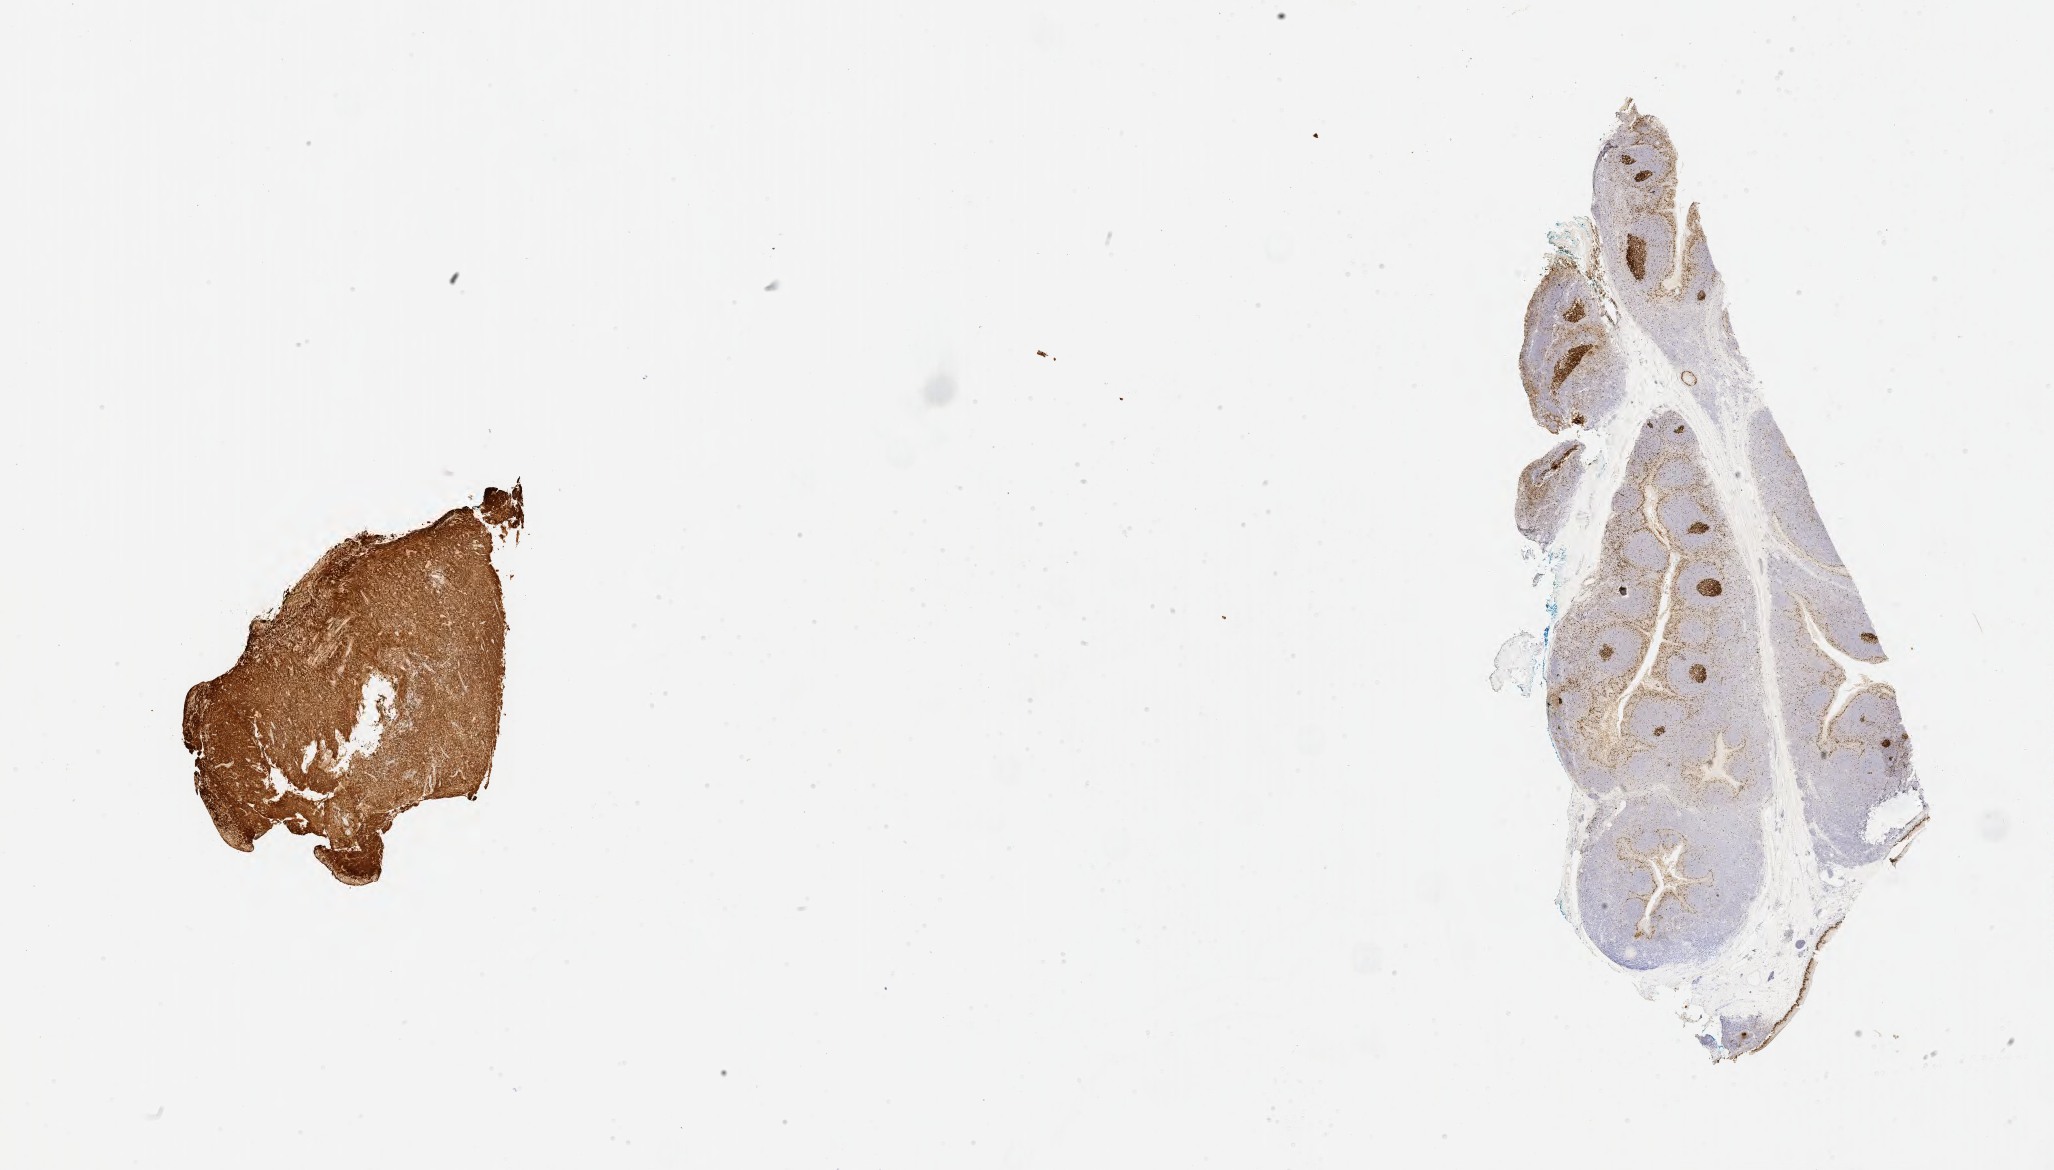
Whole-slide image, immunohistochemical stain for Ki-67, a low-resolution overview of the entire scanned area, about 33.2 x 18.9 mm. Specimen: tumor tissue. Site: ovary. Female patient; age at initial diagnosis 3 years.
• diagnosis: Burkitt lymphoma, NOS